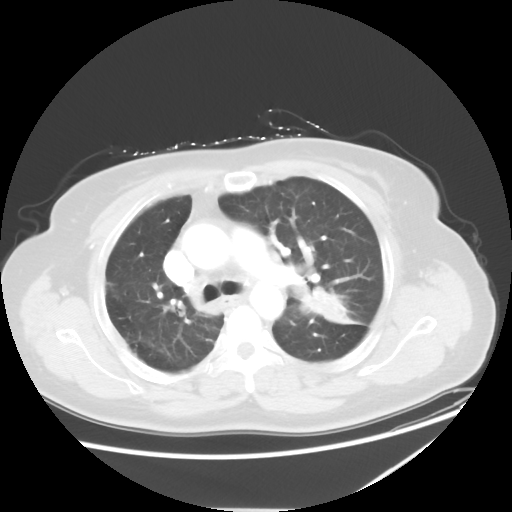
Chest CT, one axial slice. Slice 37 of 54 in the series (ordered by position). Reconstruction kernel STANDARD. 120 kVp. Lung window (W 1500 / L -600 HU). 5 mm slice thickness. 512 × 512 image matrix, field of view 384 × 384 mm. Female patient, age 61 years. From the clinical record (not read from this slice): clinical TNM (as recorded): T1c N3 M1.
Structures marked on this image (bounding box drawn by a radiologist):
- lung tumour (recorded histology: adenocarcinoma): box from (x=302, y=288) to (x=362, y=331) px